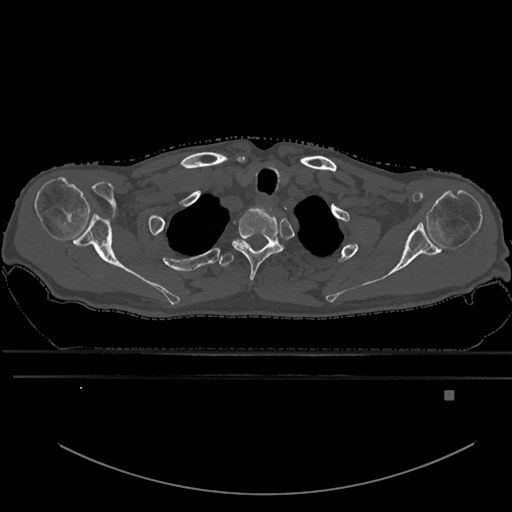
CT including the spine, one axial slice; slice 530 of 969 in the series (ordered by position); bone window (W 1800 / L 400 HU); 512 × 512 image matrix, field of view 456 × 456 mm. Patient: male, 82 years. Case-level facts recorded for this patient, not image findings: primary cancer: prostate; vertebrae with lytic lesions (as recorded): T11, T9, T8, T2.
Annotated regions visible in this slice (semi-automatic segmentation, software-assisted and operator-edited):
- T1 vertebra: bounding box <232,208,282,281> (left, top, right, bottom; pixels)
- T2 vertebra: <219,239,279,267>